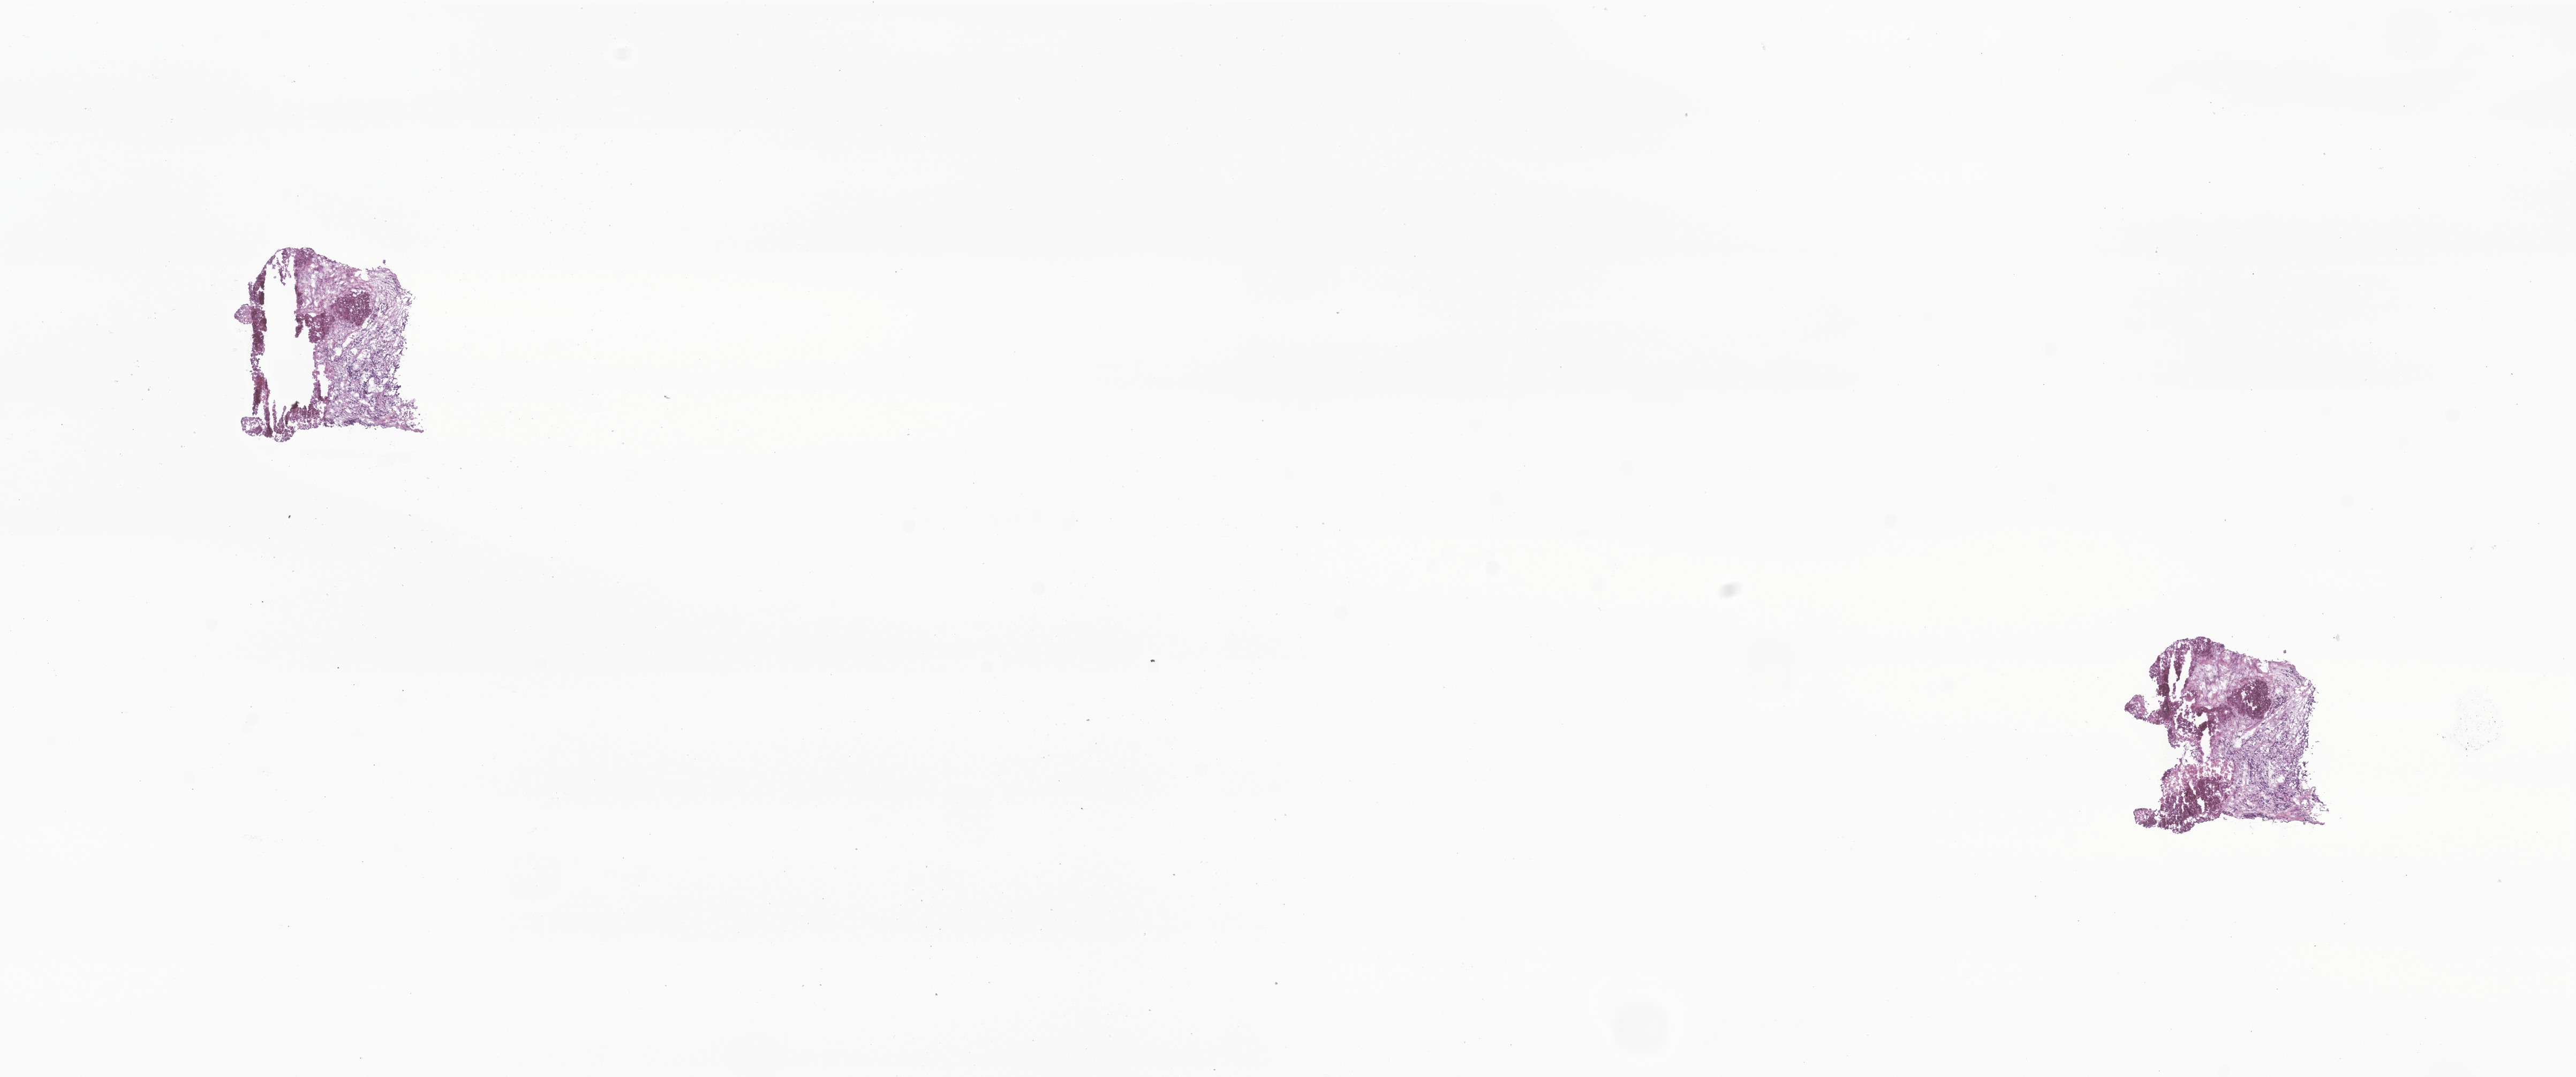
Haematoxylin and eosin whole-slide image of tumor tissue from the adrenal gland, whole scanned area (about 20.3 x 8.5 mm) shown as a low-resolution overview. Frozen section. Male patient, age 417 days (about 1.1 years).
Diagnosis: Neuroblastoma, NOS.